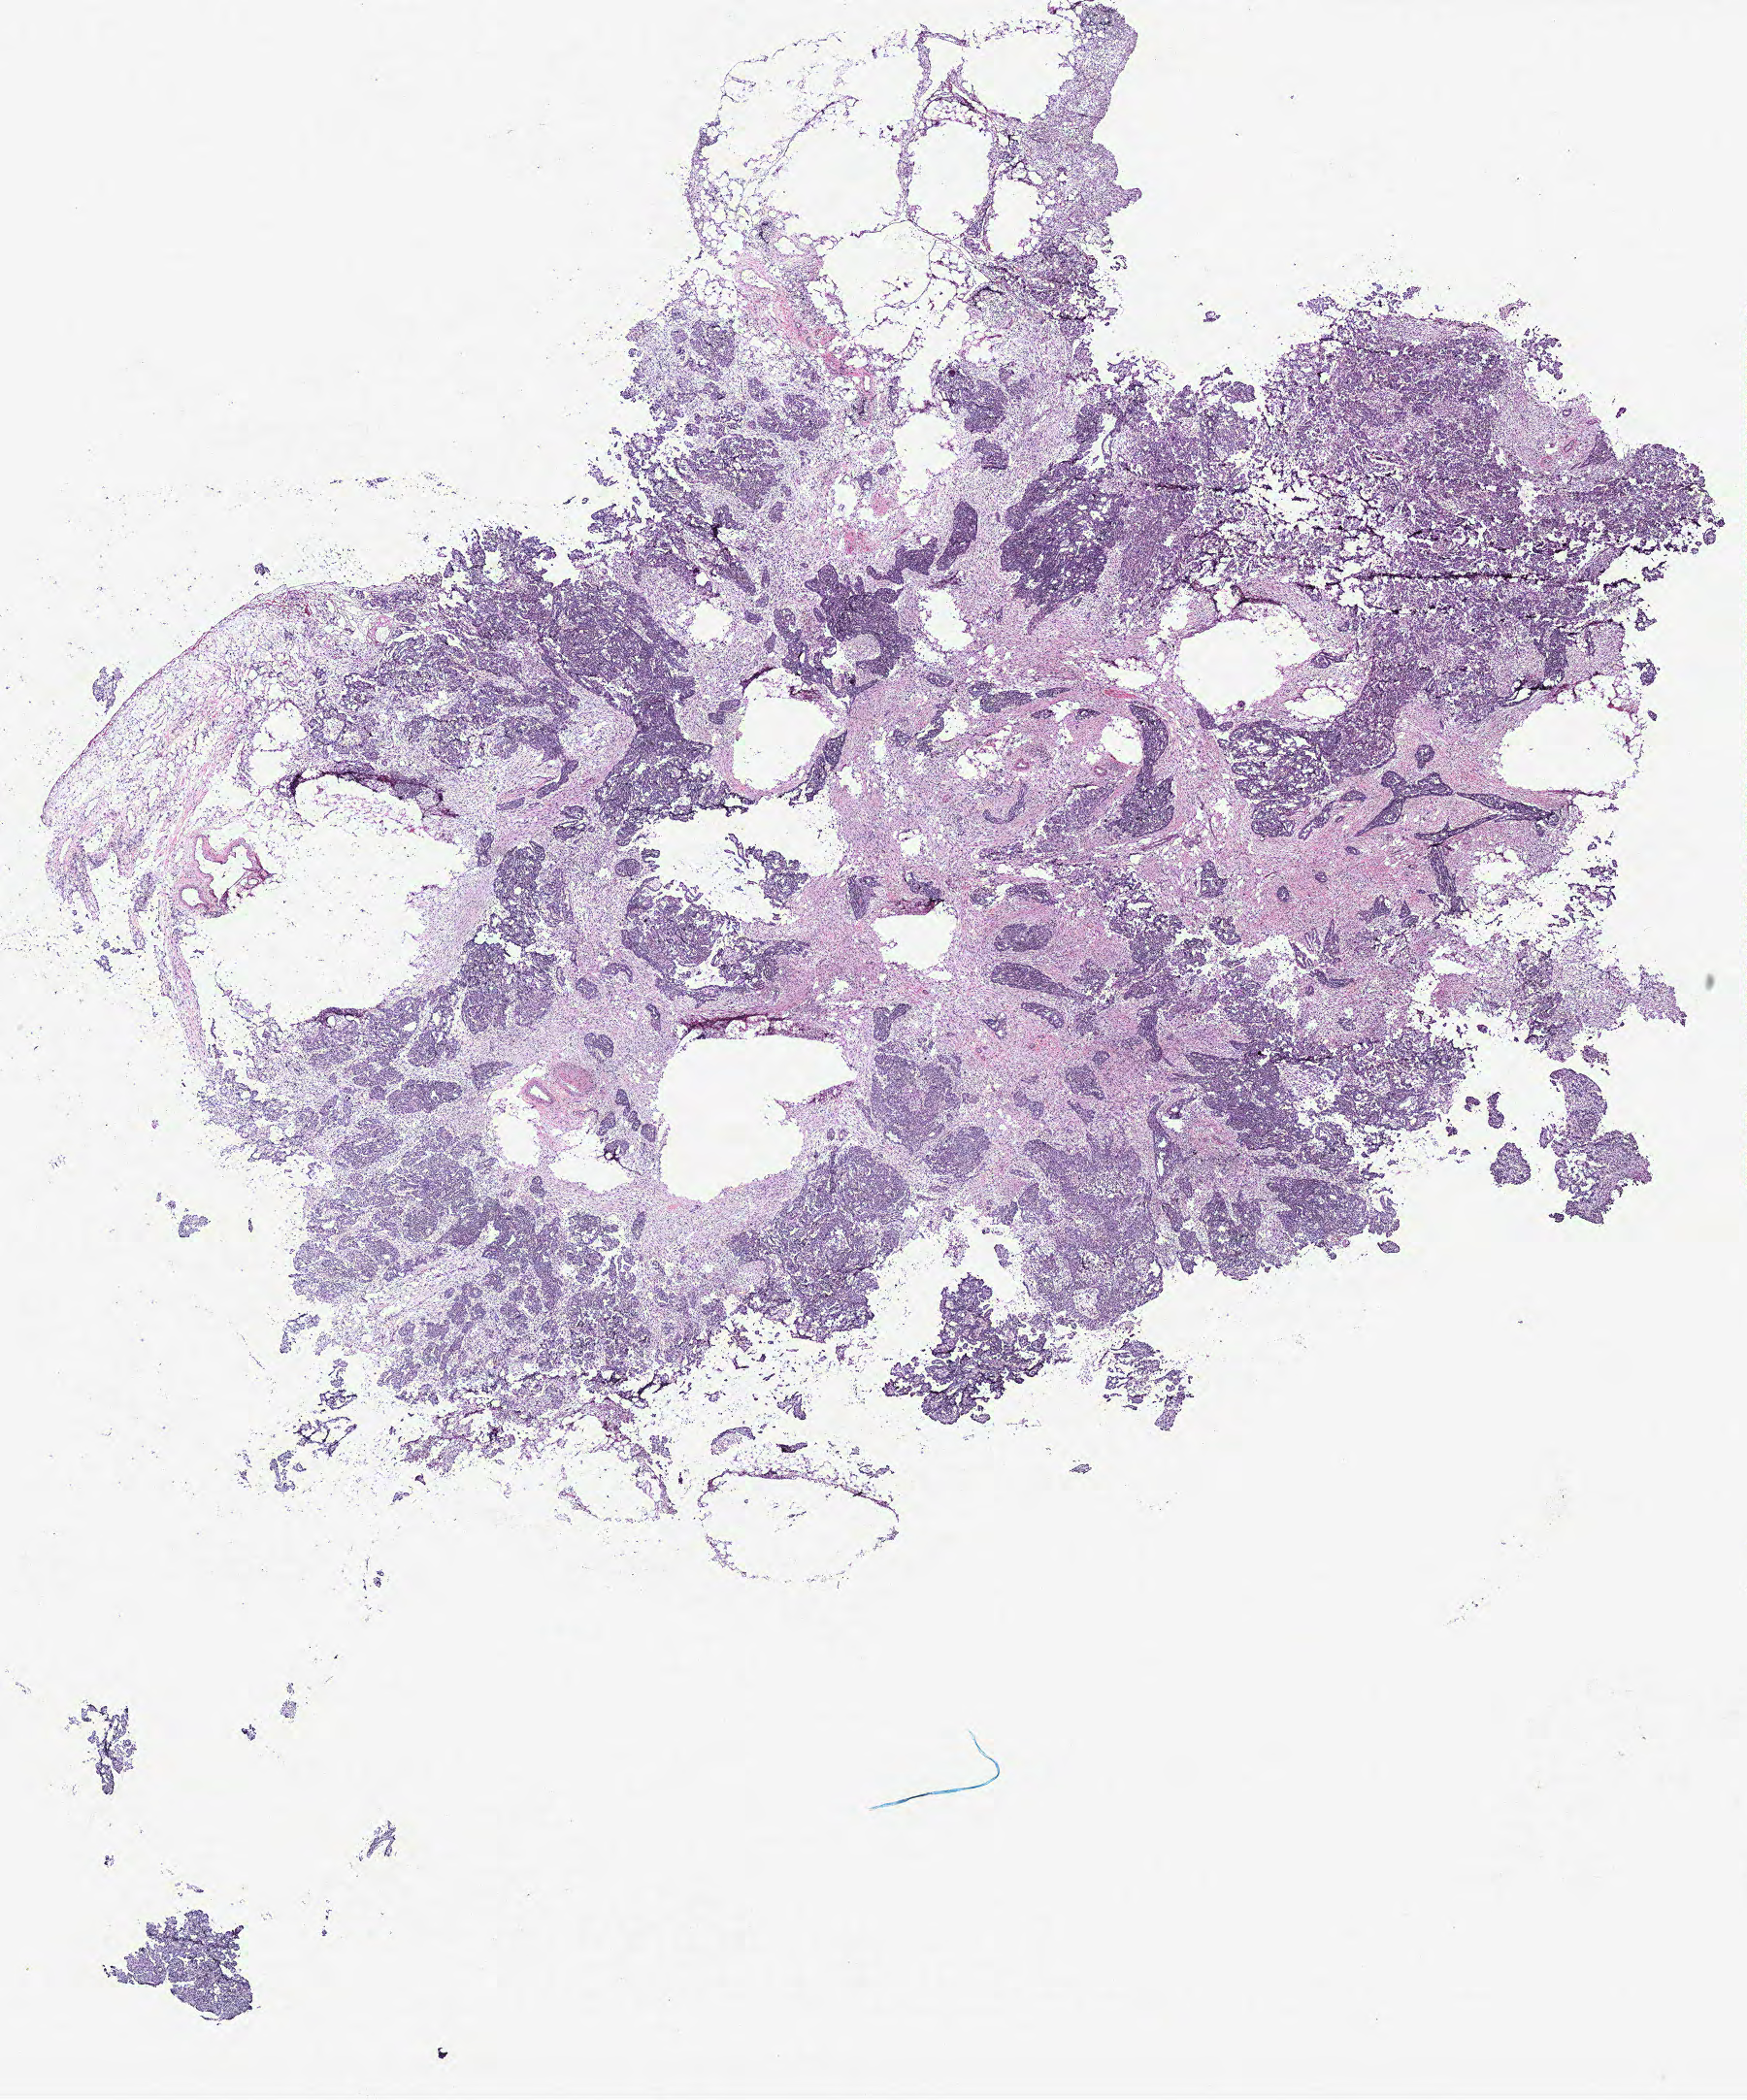
Digitized H&E tissue section (whole slide) — low-resolution overview of the scanned area, about 14.4 x 17.3 mm (slide scanned at 40x), ovary, tumour tissue. Female, 59 y/o.
Primary tumour site (as recorded): fallopian tube. Histologic diagnosis: Serous adenocarcinoma, NOS (fallopian tube).